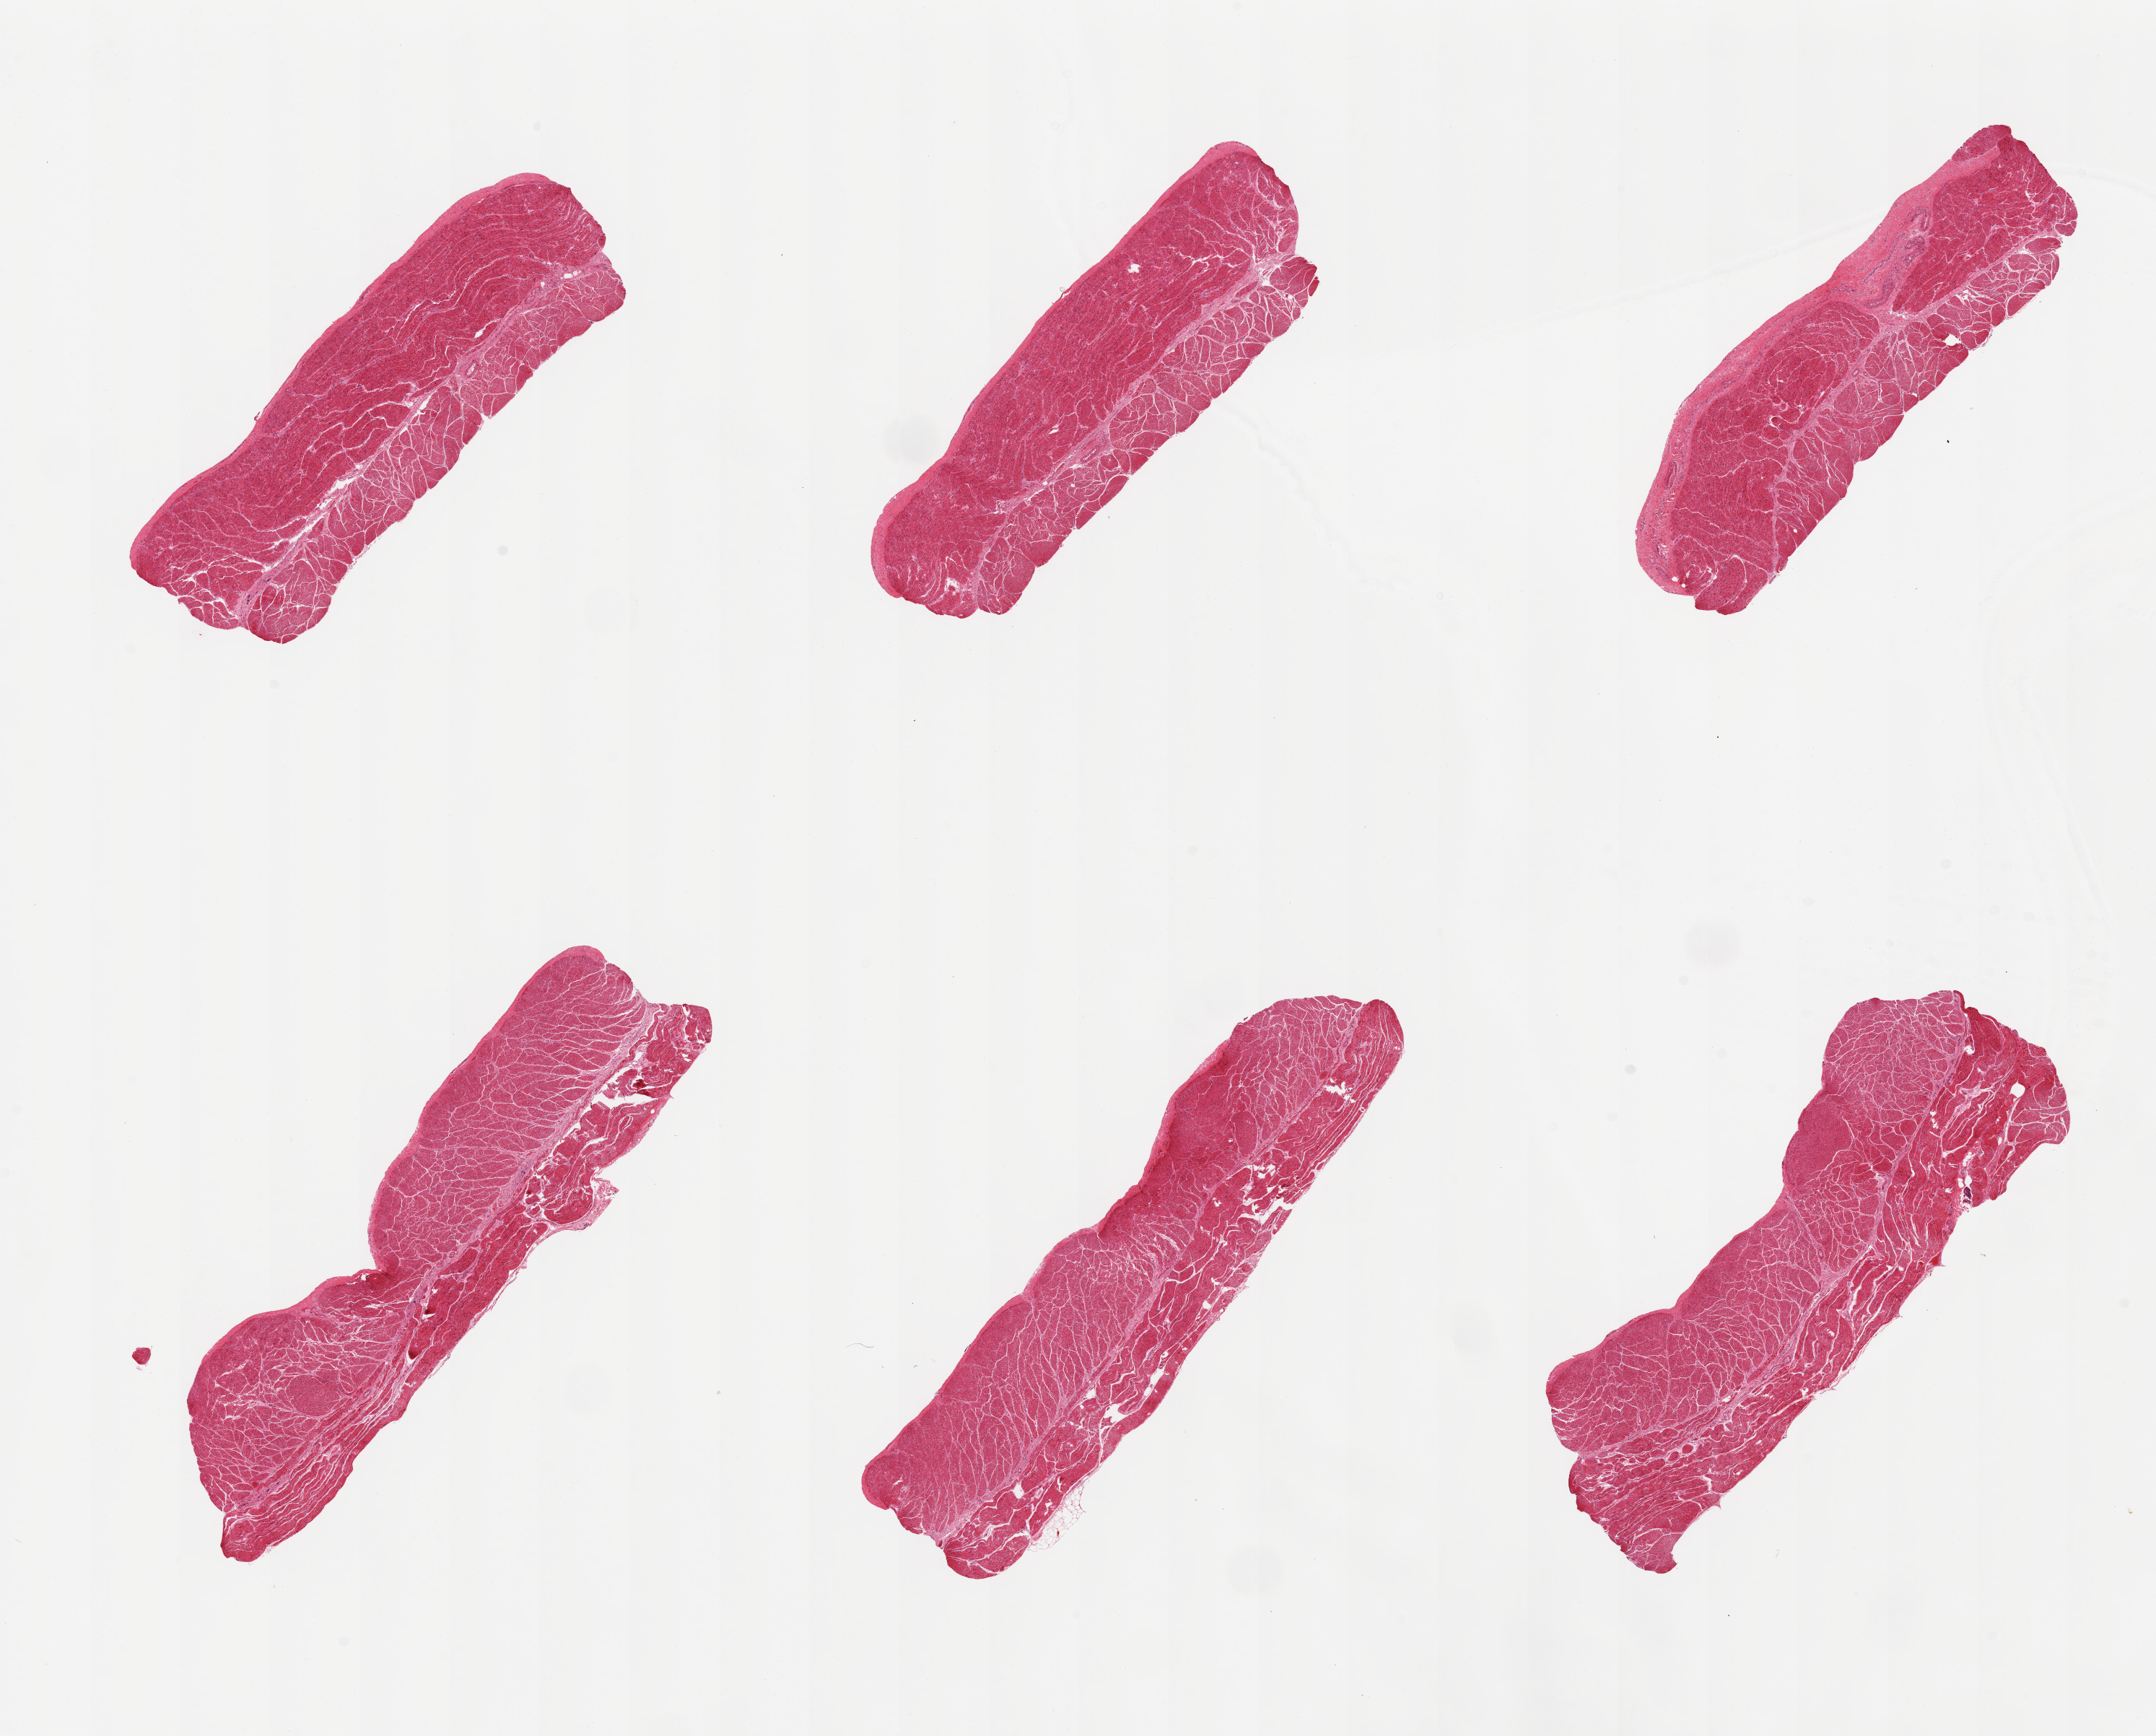
Whole-slide image, haematoxylin and eosin stain — low-resolution overview of the scanned area, about 23.6 x 19.0 mm, PAXgene-fixed paraffin-embedded (PFPE) section, target tissue: esophageal muscle, tissue donor sample. Donor sex: male.
Pathologist's review note for this sample: 6 pieces; very well trimmed.